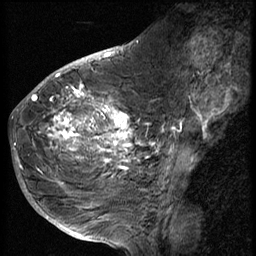
Breast MRI (dynamic contrast-enhanced), one sagittal slice; slice 25 of 56 in the series (ordered by position); 3 images stored at this slice position (order not interpretable as contrast timing); 1.5 T; TE 4.2 ms, TR 9 ms; 2.5 mm slice thickness; 256 × 256 image matrix, field of view 180 × 180 mm. Patient: female, 49 years. From the clinical record (not read from this slice): setting: breast cancer imaged before/during neoadjuvant chemotherapy; receptor status: HER2-positive.
Outlined on this slice (semi-automatic segmentation, software-assisted and operator-edited):
- analysis volume of interest (the breast-tissue region the enhancement analysis was run in; not a lesion): bounding box [x1, y1, x2, y2] px = [37, 85, 138, 207]
- tumour enhancement mask (voxels above the 140 % enhancement threshold inside the analysis volume of interest): [47, 86, 137, 179]